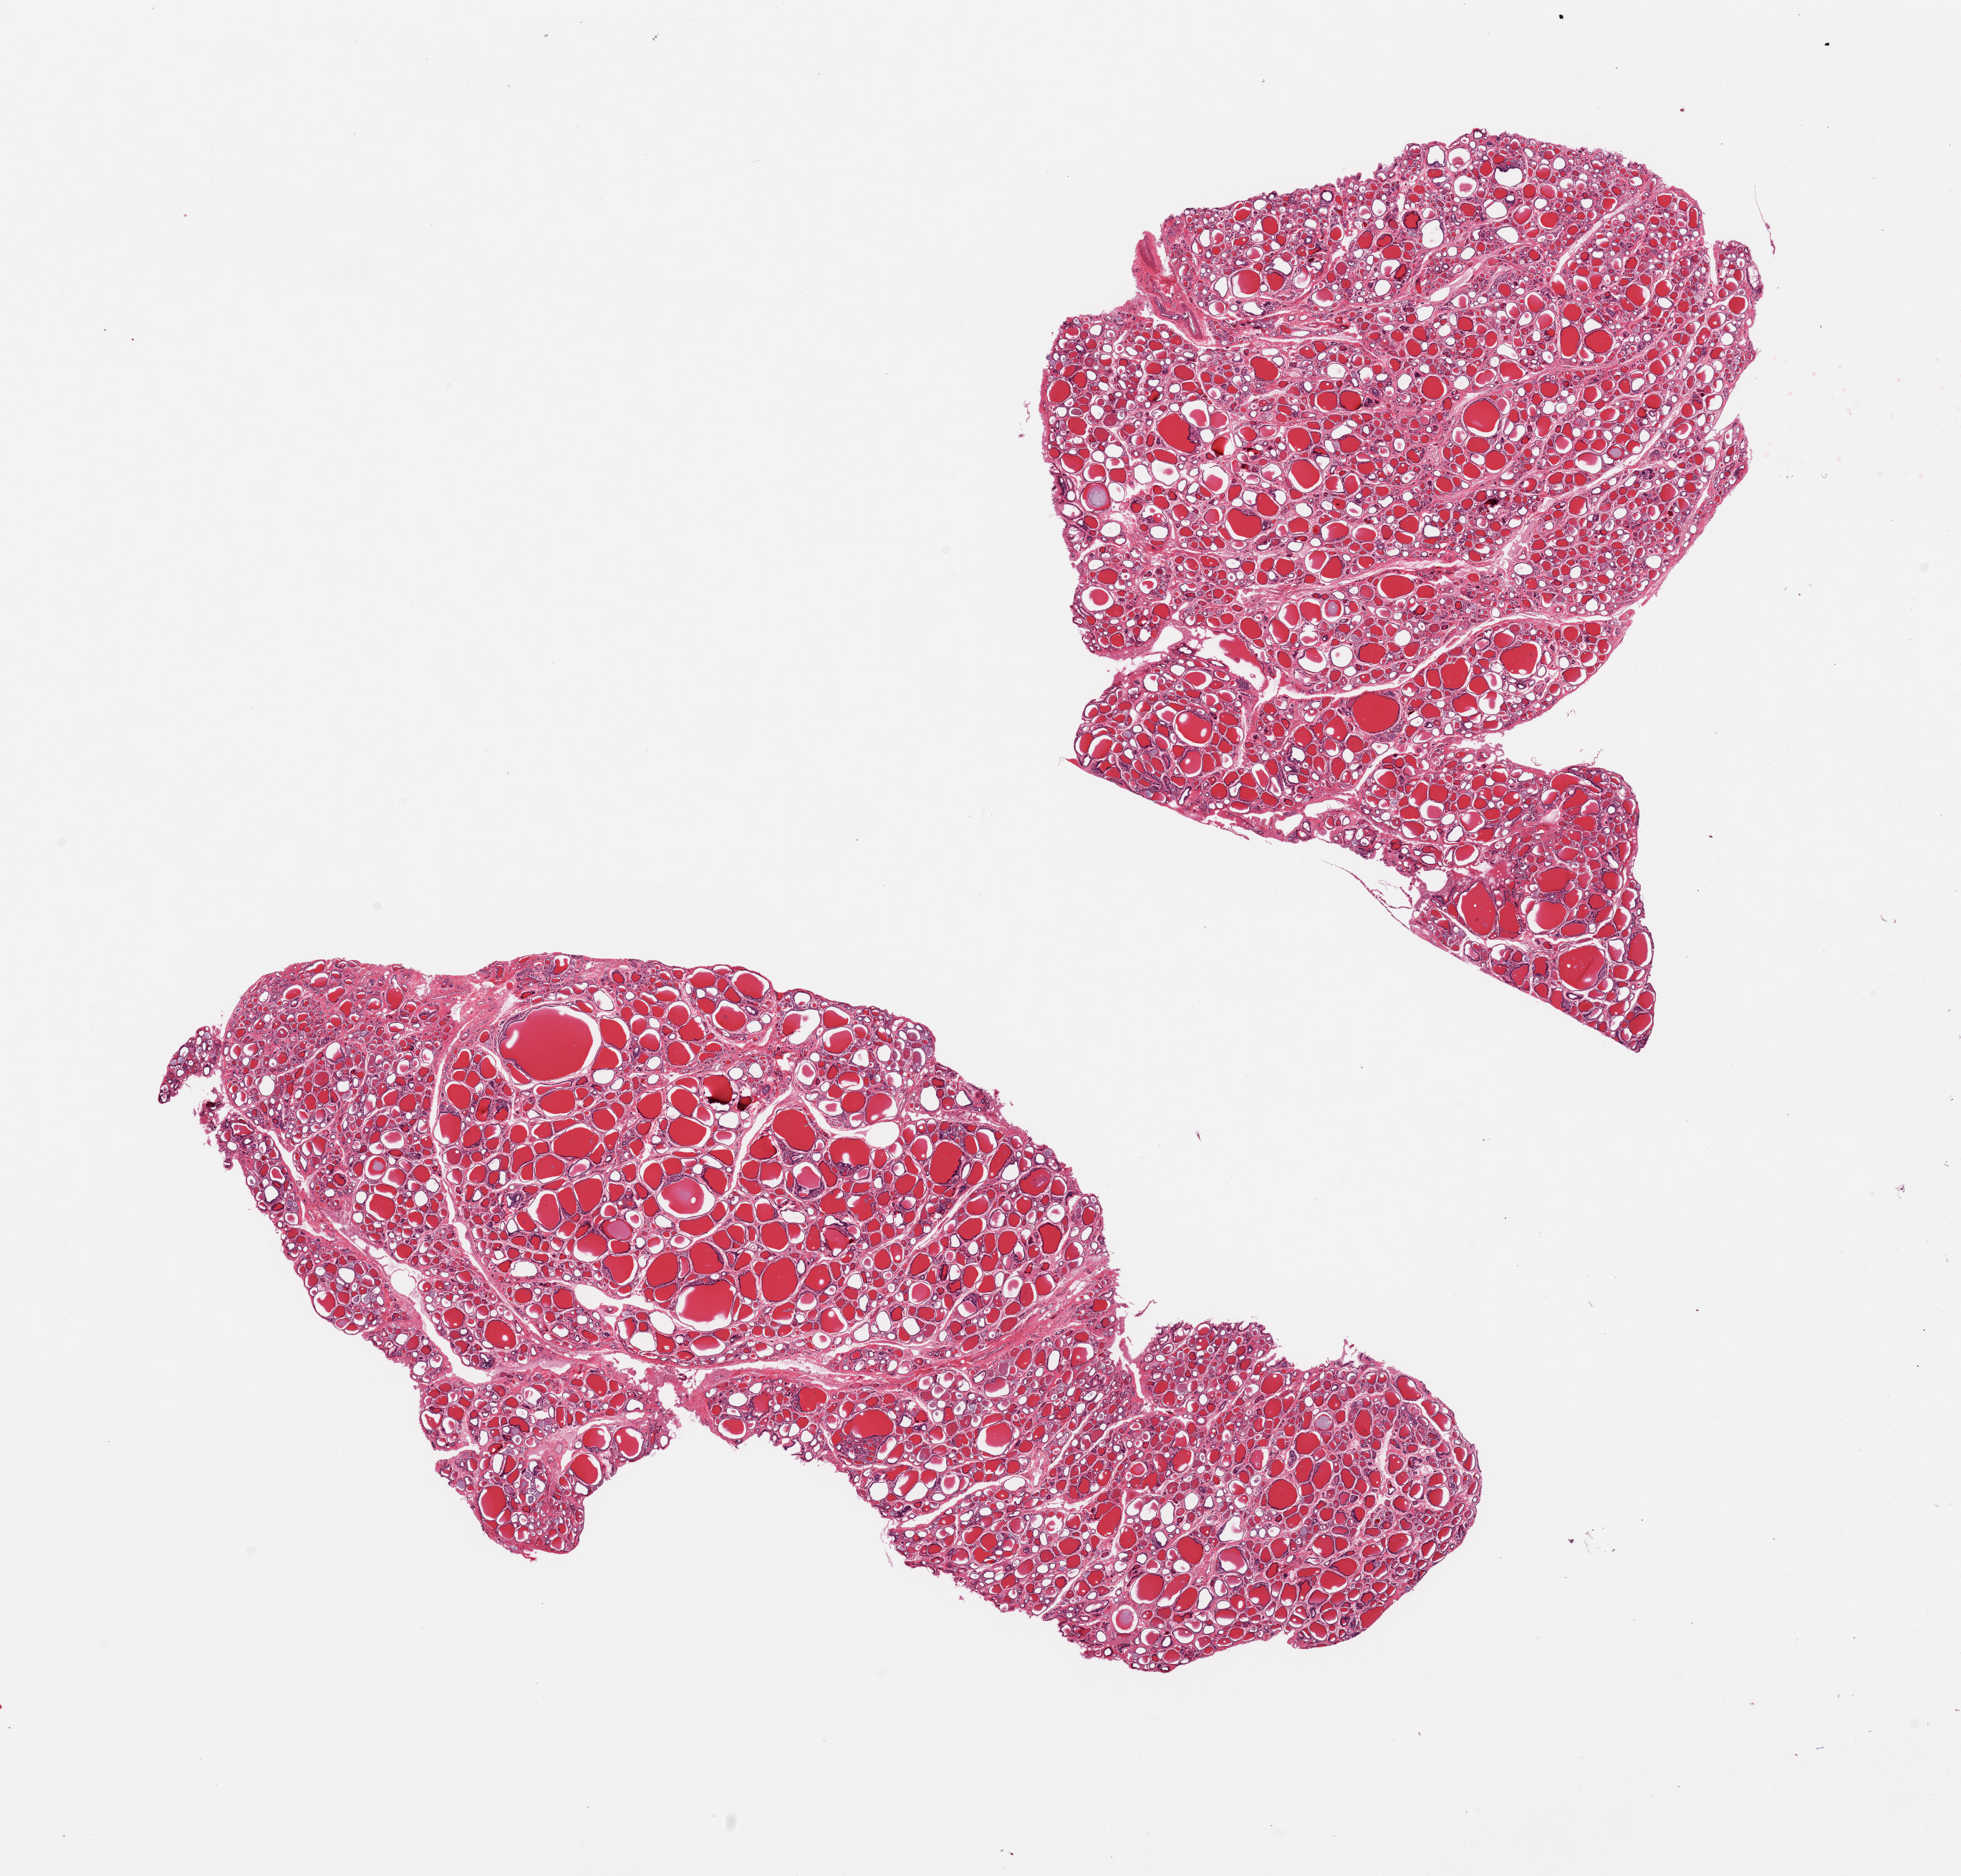
H&E whole-slide image — a low-resolution overview of the entire scanned area, about 21.7 x 20.7 mm (slide scanned at 20x); PAXgene-fixed paraffin-embedded (PFPE) section; sampled site (target tissue): thyroid; donor tissue sample. Donor: female.
• reviewer comment on this tissue sample: 2 pieces, features of mulinodular goitre